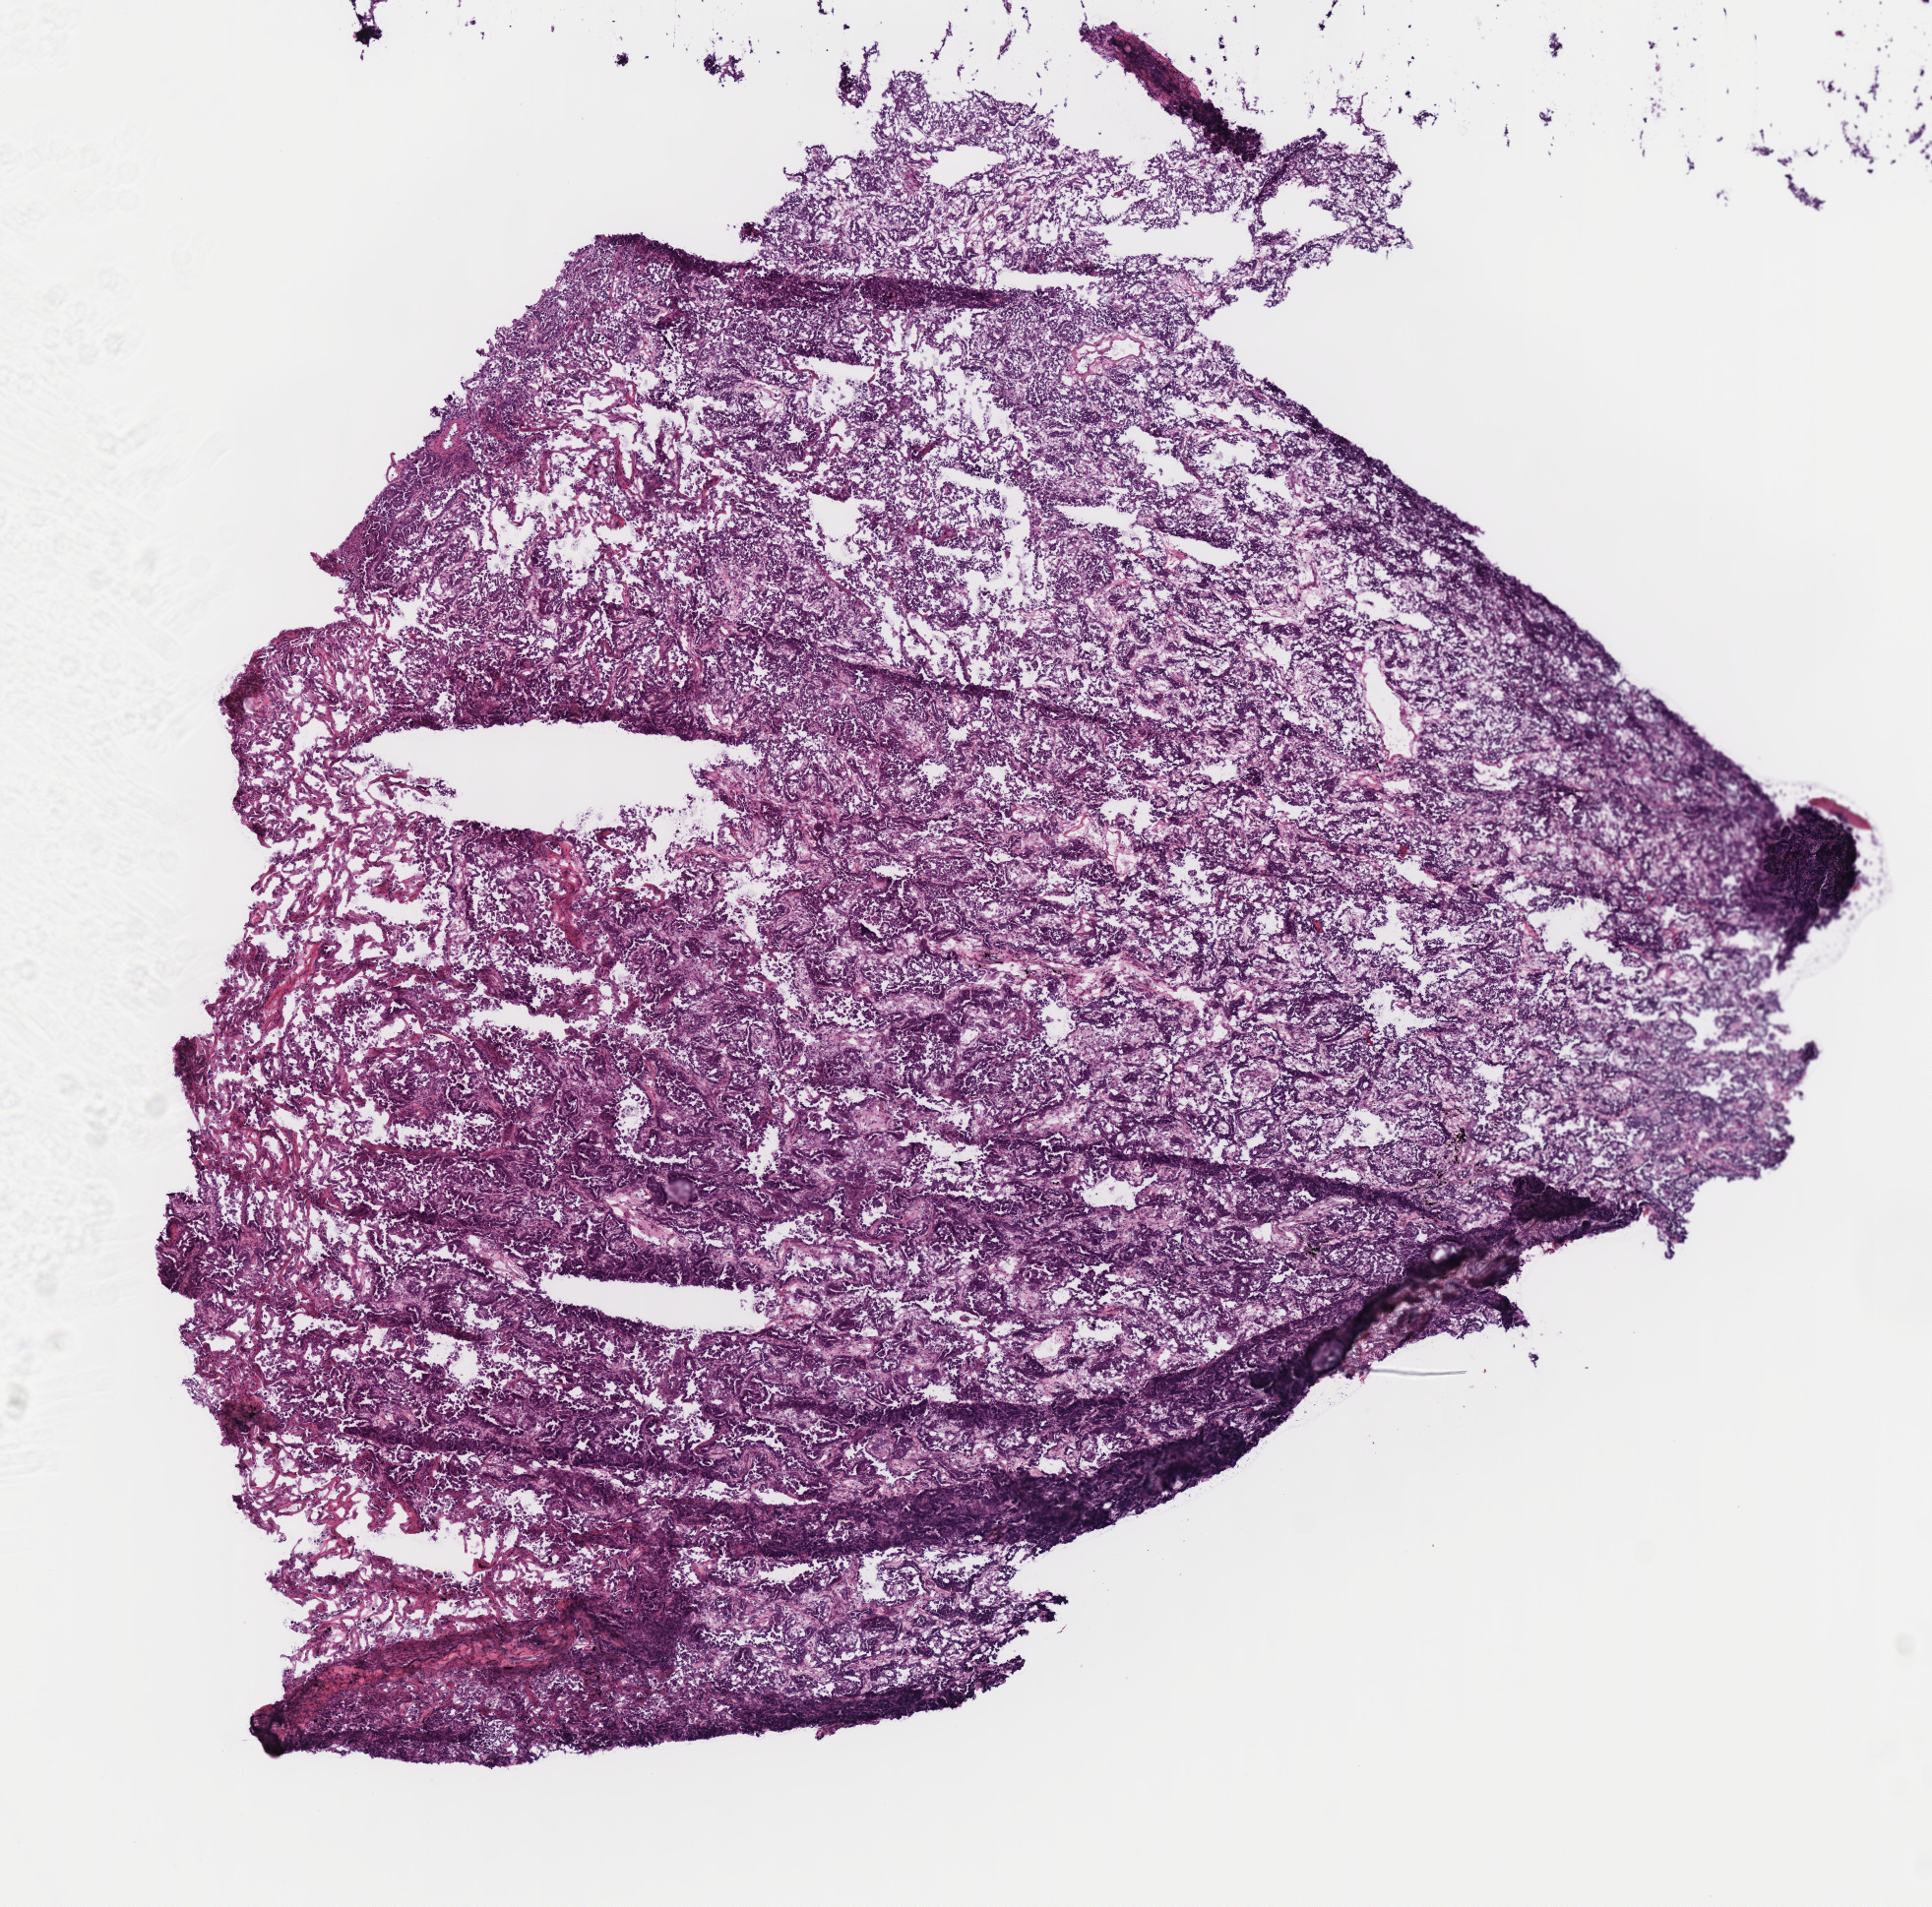
Whole-slide histology image, H&E-stained, shown as a low-resolution overview of the whole scanned area (about 7.7 x 7.6 mm, acquisition: 40x scan), frozen section from the top of the tissue portion, lung, primary tumour sample. Patient: male, age at initial diagnosis 67 years. Composition of this section per pathologist review: tumour cells 80%, tumour nuclei 75%, normal cells 10%, stromal cells 10%, necrosis 0%.
• AJCC pathologic stage: IB (6th edition)
• histologic diagnosis: Adenocarcinoma with mixed subtypes (upper lobe, lung)
• TNM: T2 N0 M0